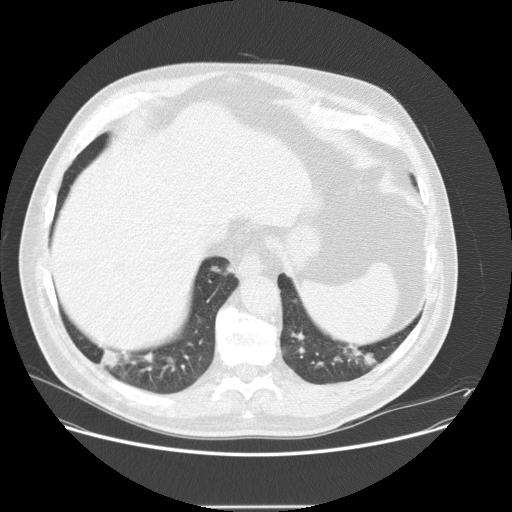
Chest CT (low-dose screening protocol), one axial image; baseline screening round; lung window (W 1500 / L -600 HU); 2.5 mm slice thickness; slice 106 of 143 in the series; 512 × 512 image matrix, field of view 400 × 400 mm. Male participant, aged 61 years at enrolment. Current smoker at enrolment.
2 expert reader's lesion annotations on this slice (largest first), bounding box (x1, y1, x2, y2) in pixels: (91, 338, 146, 388); (199, 254, 242, 293). The screening reader recorded 2 non-calcified nodules or masses ≥4 mm on this exam (left lower lobe, right lower lobe); which of them these boxes mark is not recorded. Official screen result: positive, change unspecified: nodule(s) >= 4 mm or enlarging nodule(s), mass(es), or other non-specific abnormalities suspicious for lung cancer. Participant outcome: lung cancer diagnosed 41 days after this screen — bronchiolo-alveolar carcinoma, mucinous, right lower lobe, well differentiated (G1), stage IV (AJCC 6th edition), 23 mm at pathology.